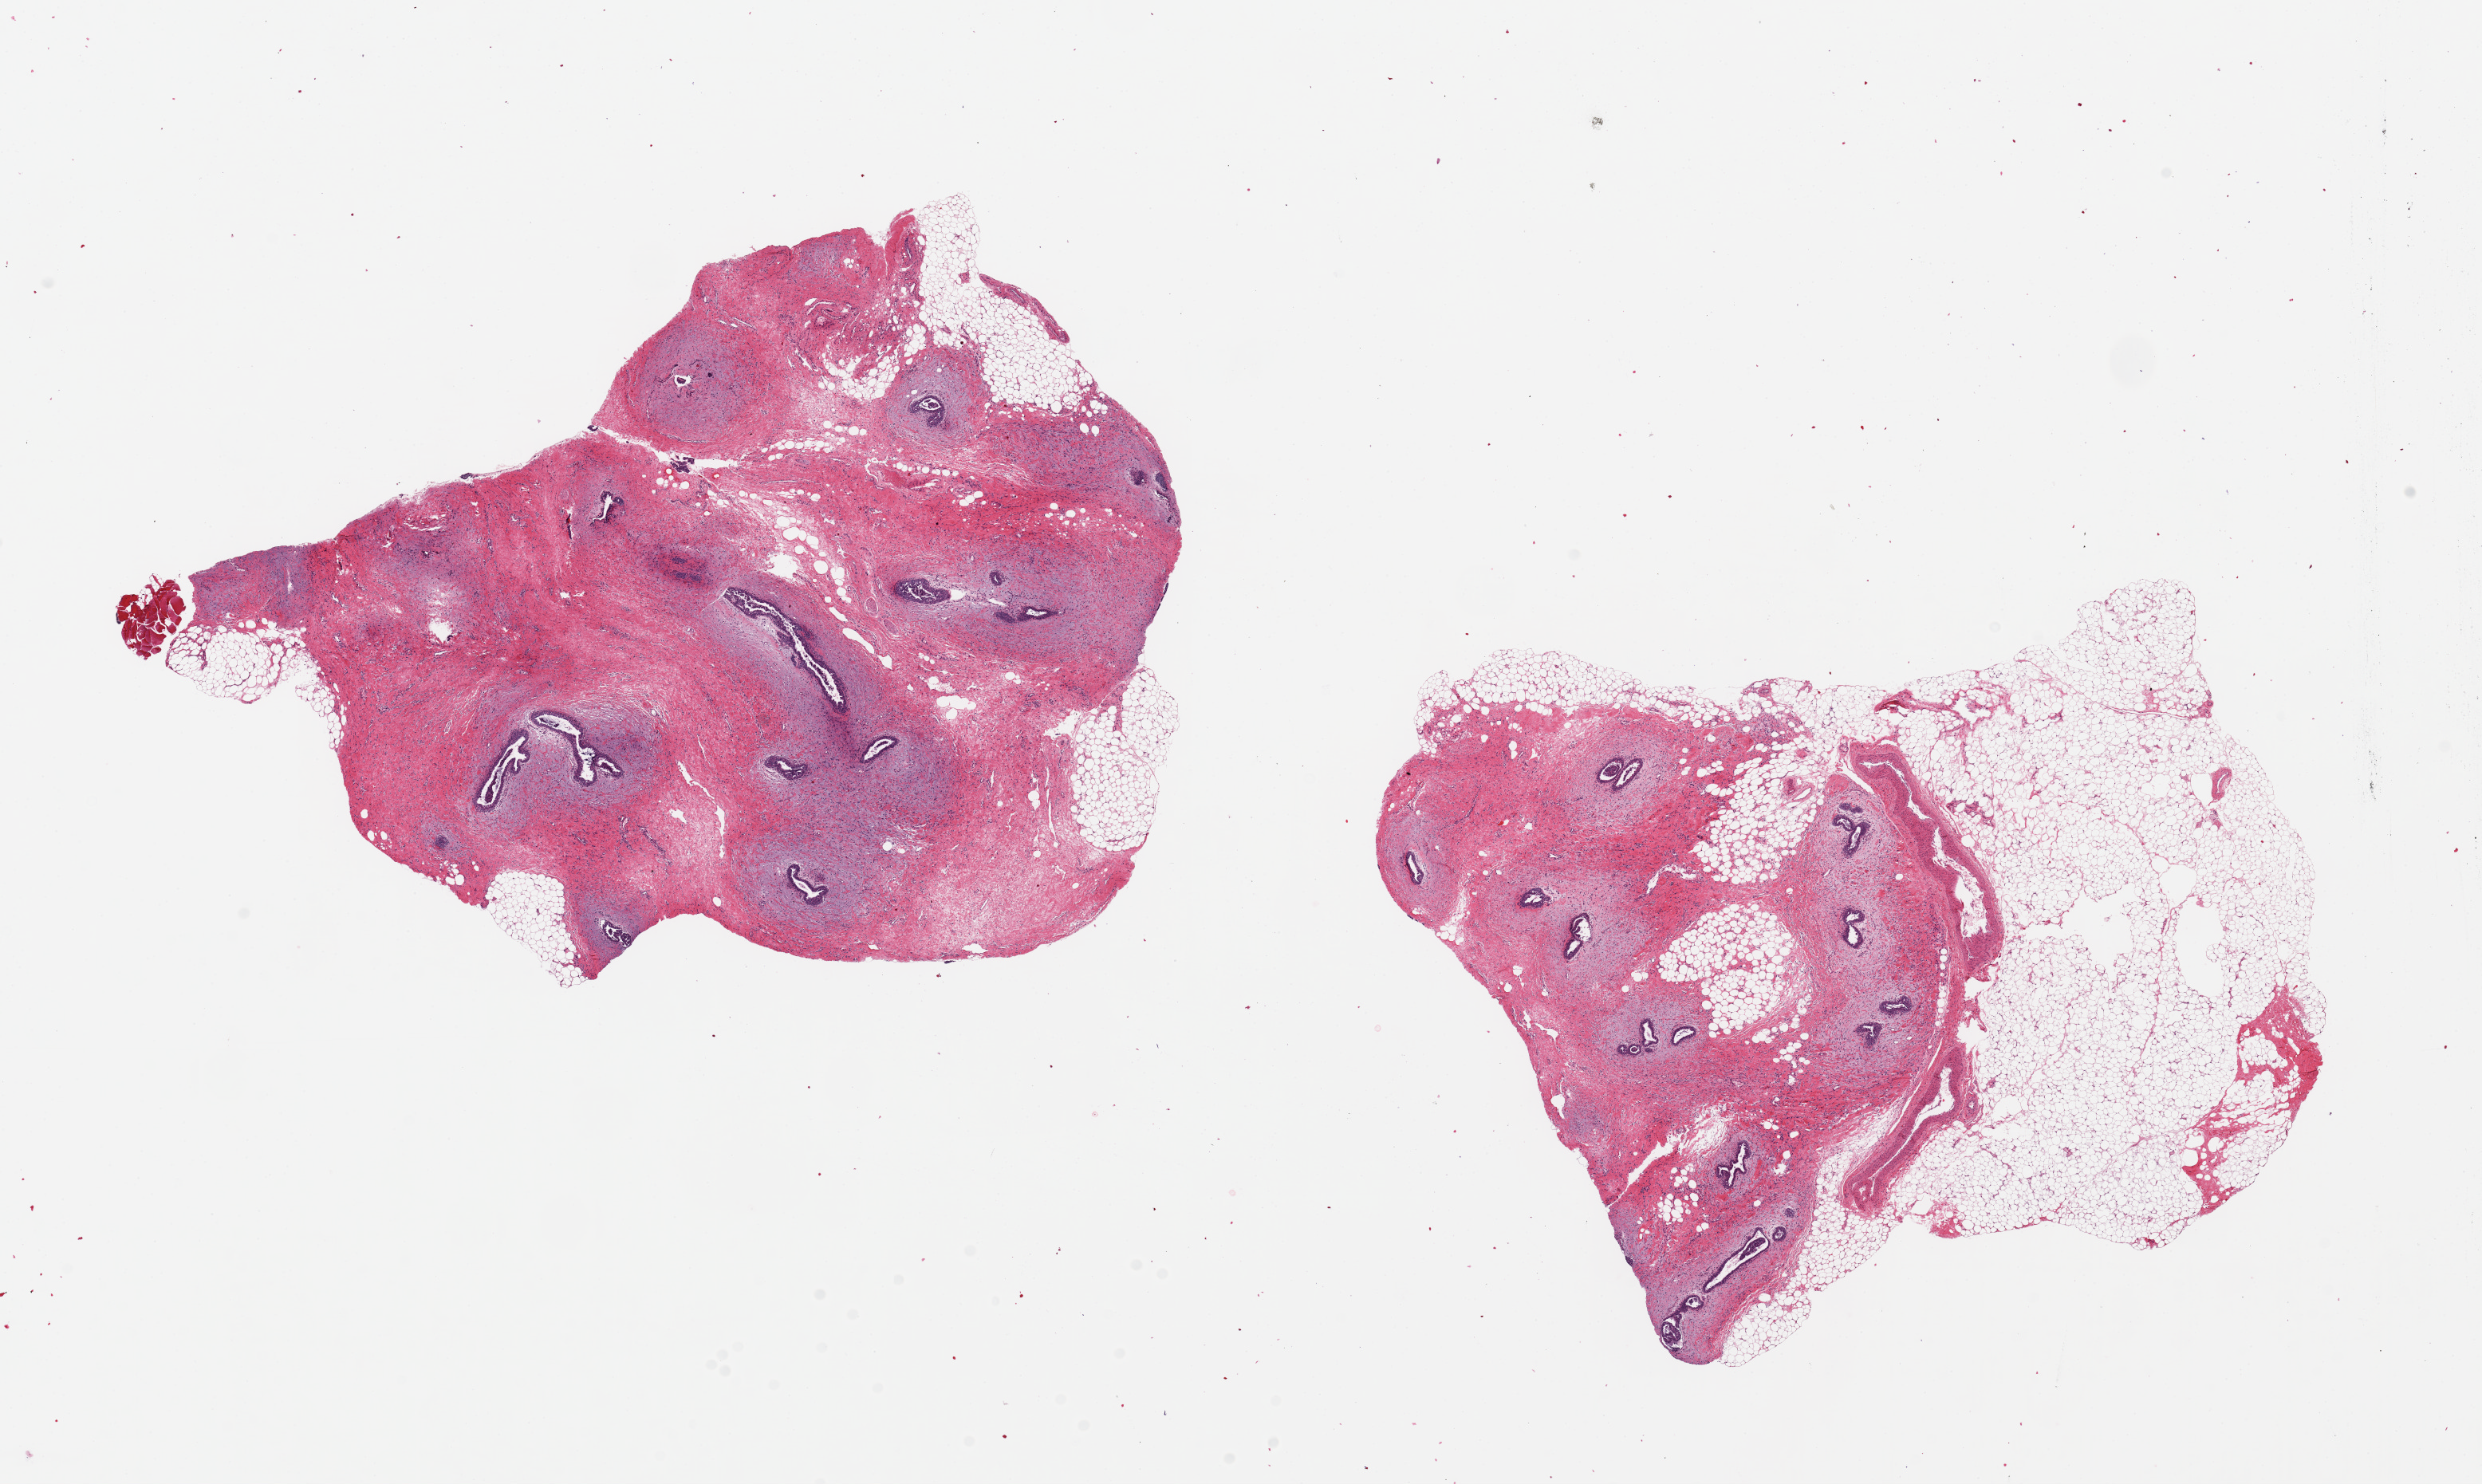
Whole-slide image, H&E stain, whole scanned area (about 24.6 x 14.7 mm, acquisition: 20x scan) shown as a low-resolution overview, PAXgene-fixed, paraffin-embedded tissue, target tissue: breast, donor tissue sample. Donor: male.
• pathologist's review note for this sample: 2 pieces, 9x8 & 9x7mm; Gynecomastia with atypical ductal hyperplasia